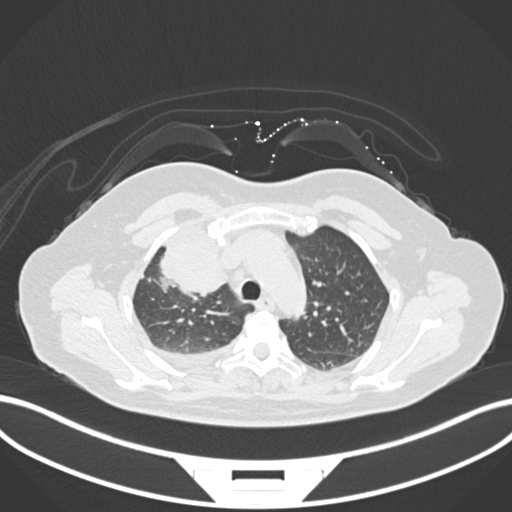
Chest CT, one axial slice. Position 121 of 172 along the scan axis. Reconstruction kernel B30f. Lung window (W 1500 / L -600 HU). 512 × 512 image matrix. Female patient, age 52 years. Case-level facts recorded for this patient, not image findings: clinical TNM (as recorded): T3 N1 M1.
Outlined on this slice (rectangle marked by the reading radiologist):
- lung tumour (recorded histology: adenocarcinoma): bounding box (x1, y1, x2, y2) in pixels: (149, 221, 230, 299)